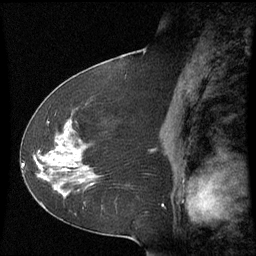
Breast MRI (dynamic contrast-enhanced), one sagittal slice; position 31 of 60 along the scan axis; dynamic contrast-enhanced series, image 2 of 3 at this slice position (ordered by acquisition); 1.5 T; TE 4.2 ms, TR 8.9 ms; 2.3 mm slice thickness; 256 × 256 image matrix, field of view 210 × 210 mm. Patient: female, 51 years. From the clinical record (not read from this slice): setting: breast cancer imaged before/during neoadjuvant chemotherapy; receptor status: HR-positive, HER2-negative.
Structures marked on this image (semi-automatically segmented with operator editing):
- analysis volume of interest (the breast-tissue region the enhancement analysis was run in; not a lesion): bounding box <50,122,100,187> (left, top, right, bottom; pixels)
- tumour enhancement mask (voxels above the 70 % enhancement threshold inside the analysis volume of interest): <52,133,83,182>